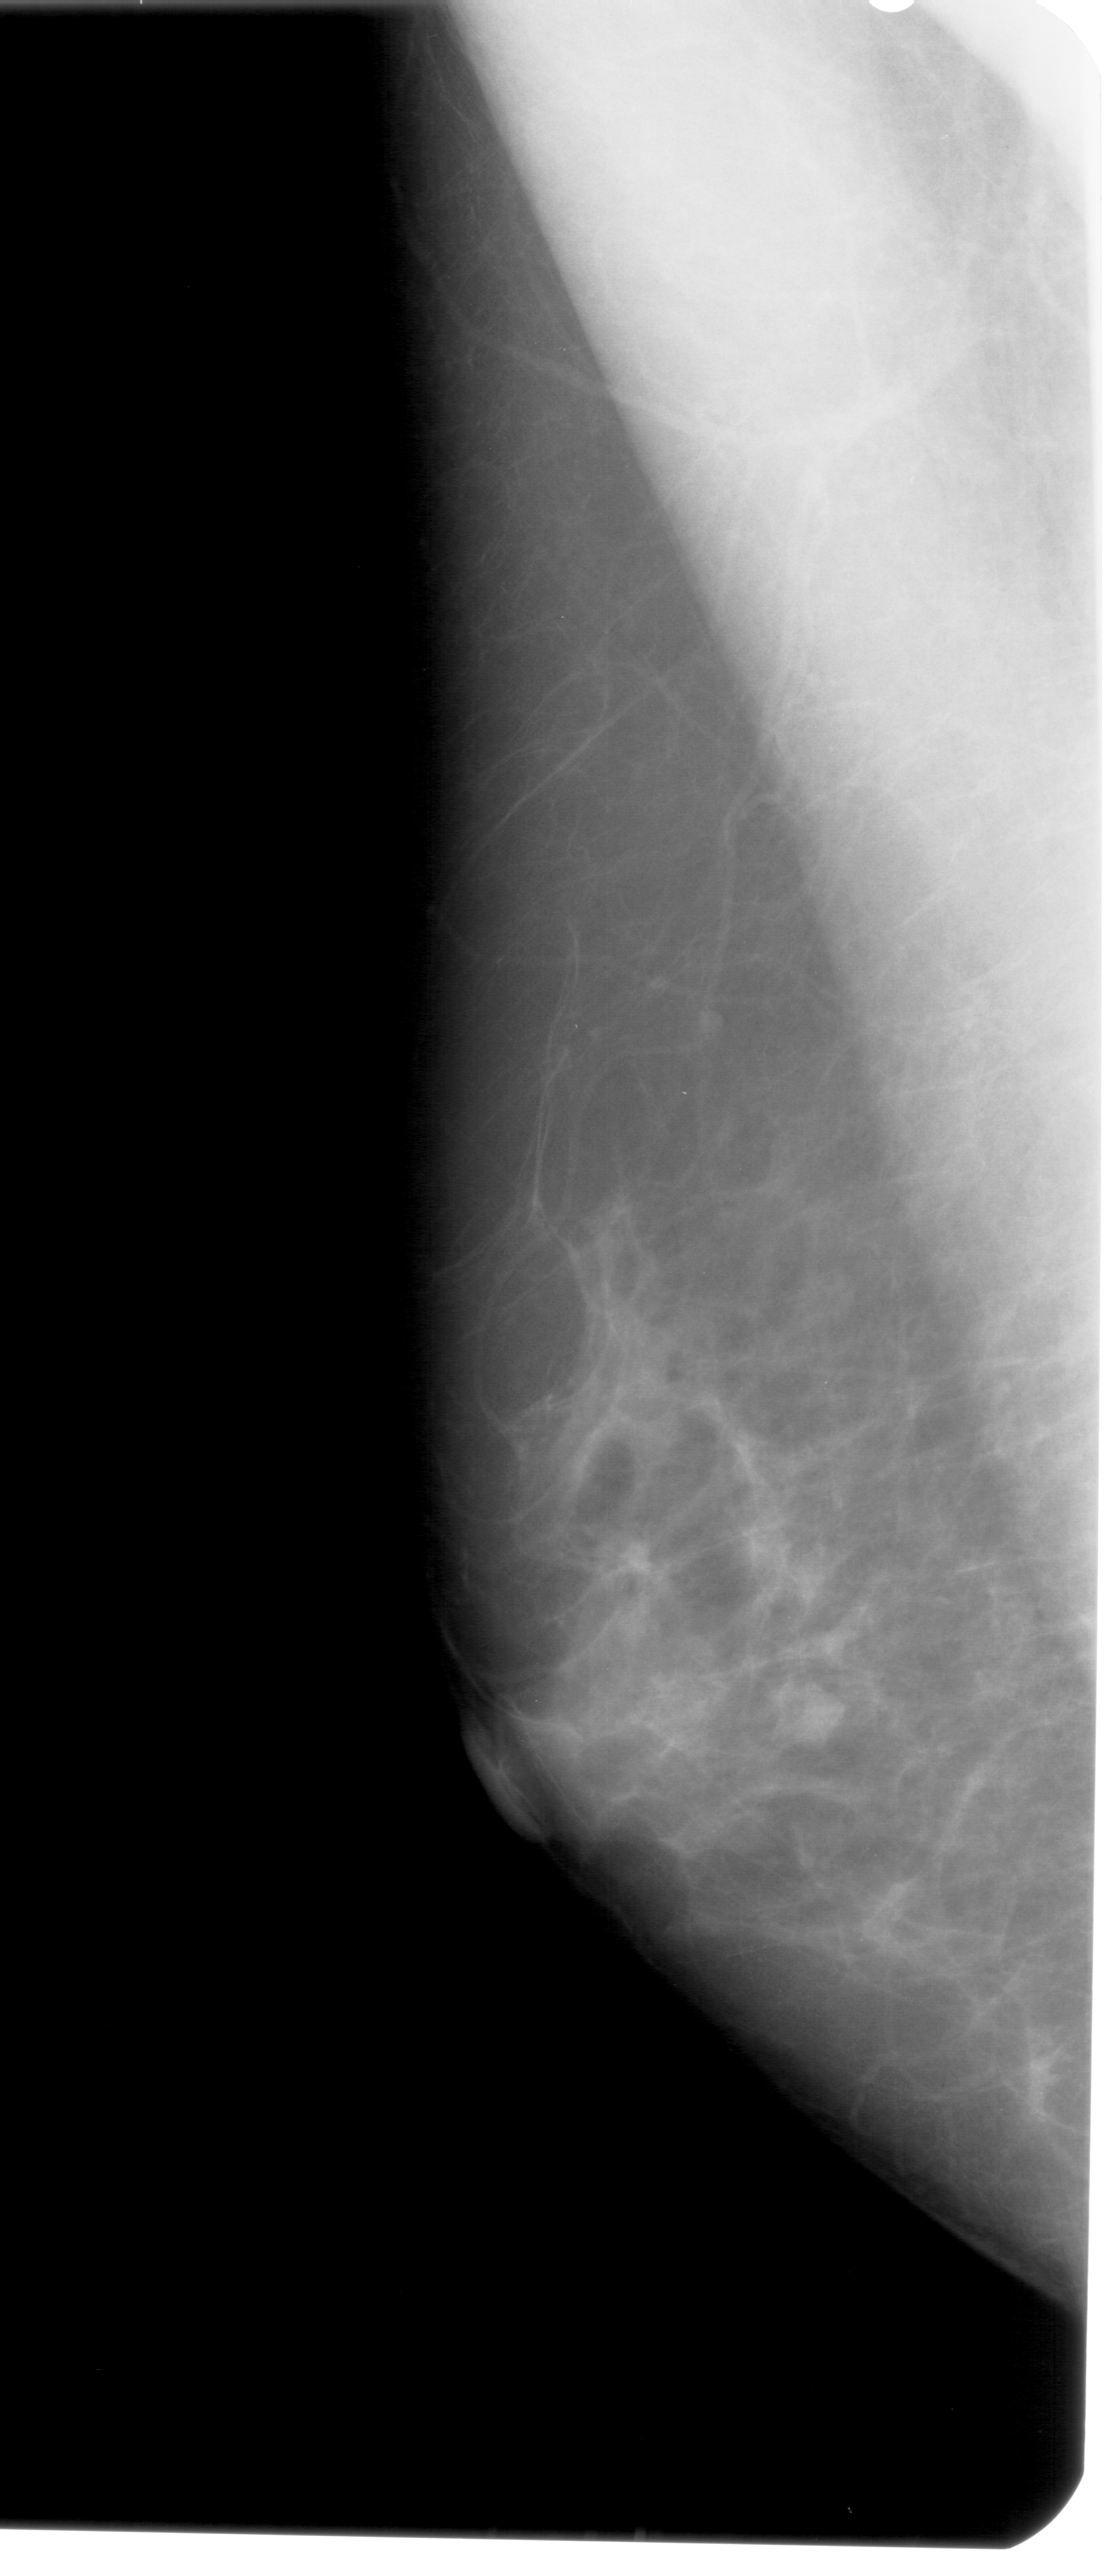
Scanned film-screen mammogram. Left breast. MLO view. BI-RADS breast density category 1 (scale 1–4). 1105 × 2576 image matrix.
Expert-marked regions of interest on this image (one box per marked abnormality):
- mass, shape lobulated, margins obscured; BI-RADS assessment category 4; pathology result (as recorded, not read from the image): benign: bounding box <762,1674,851,1753> (left, top, right, bottom; pixels)